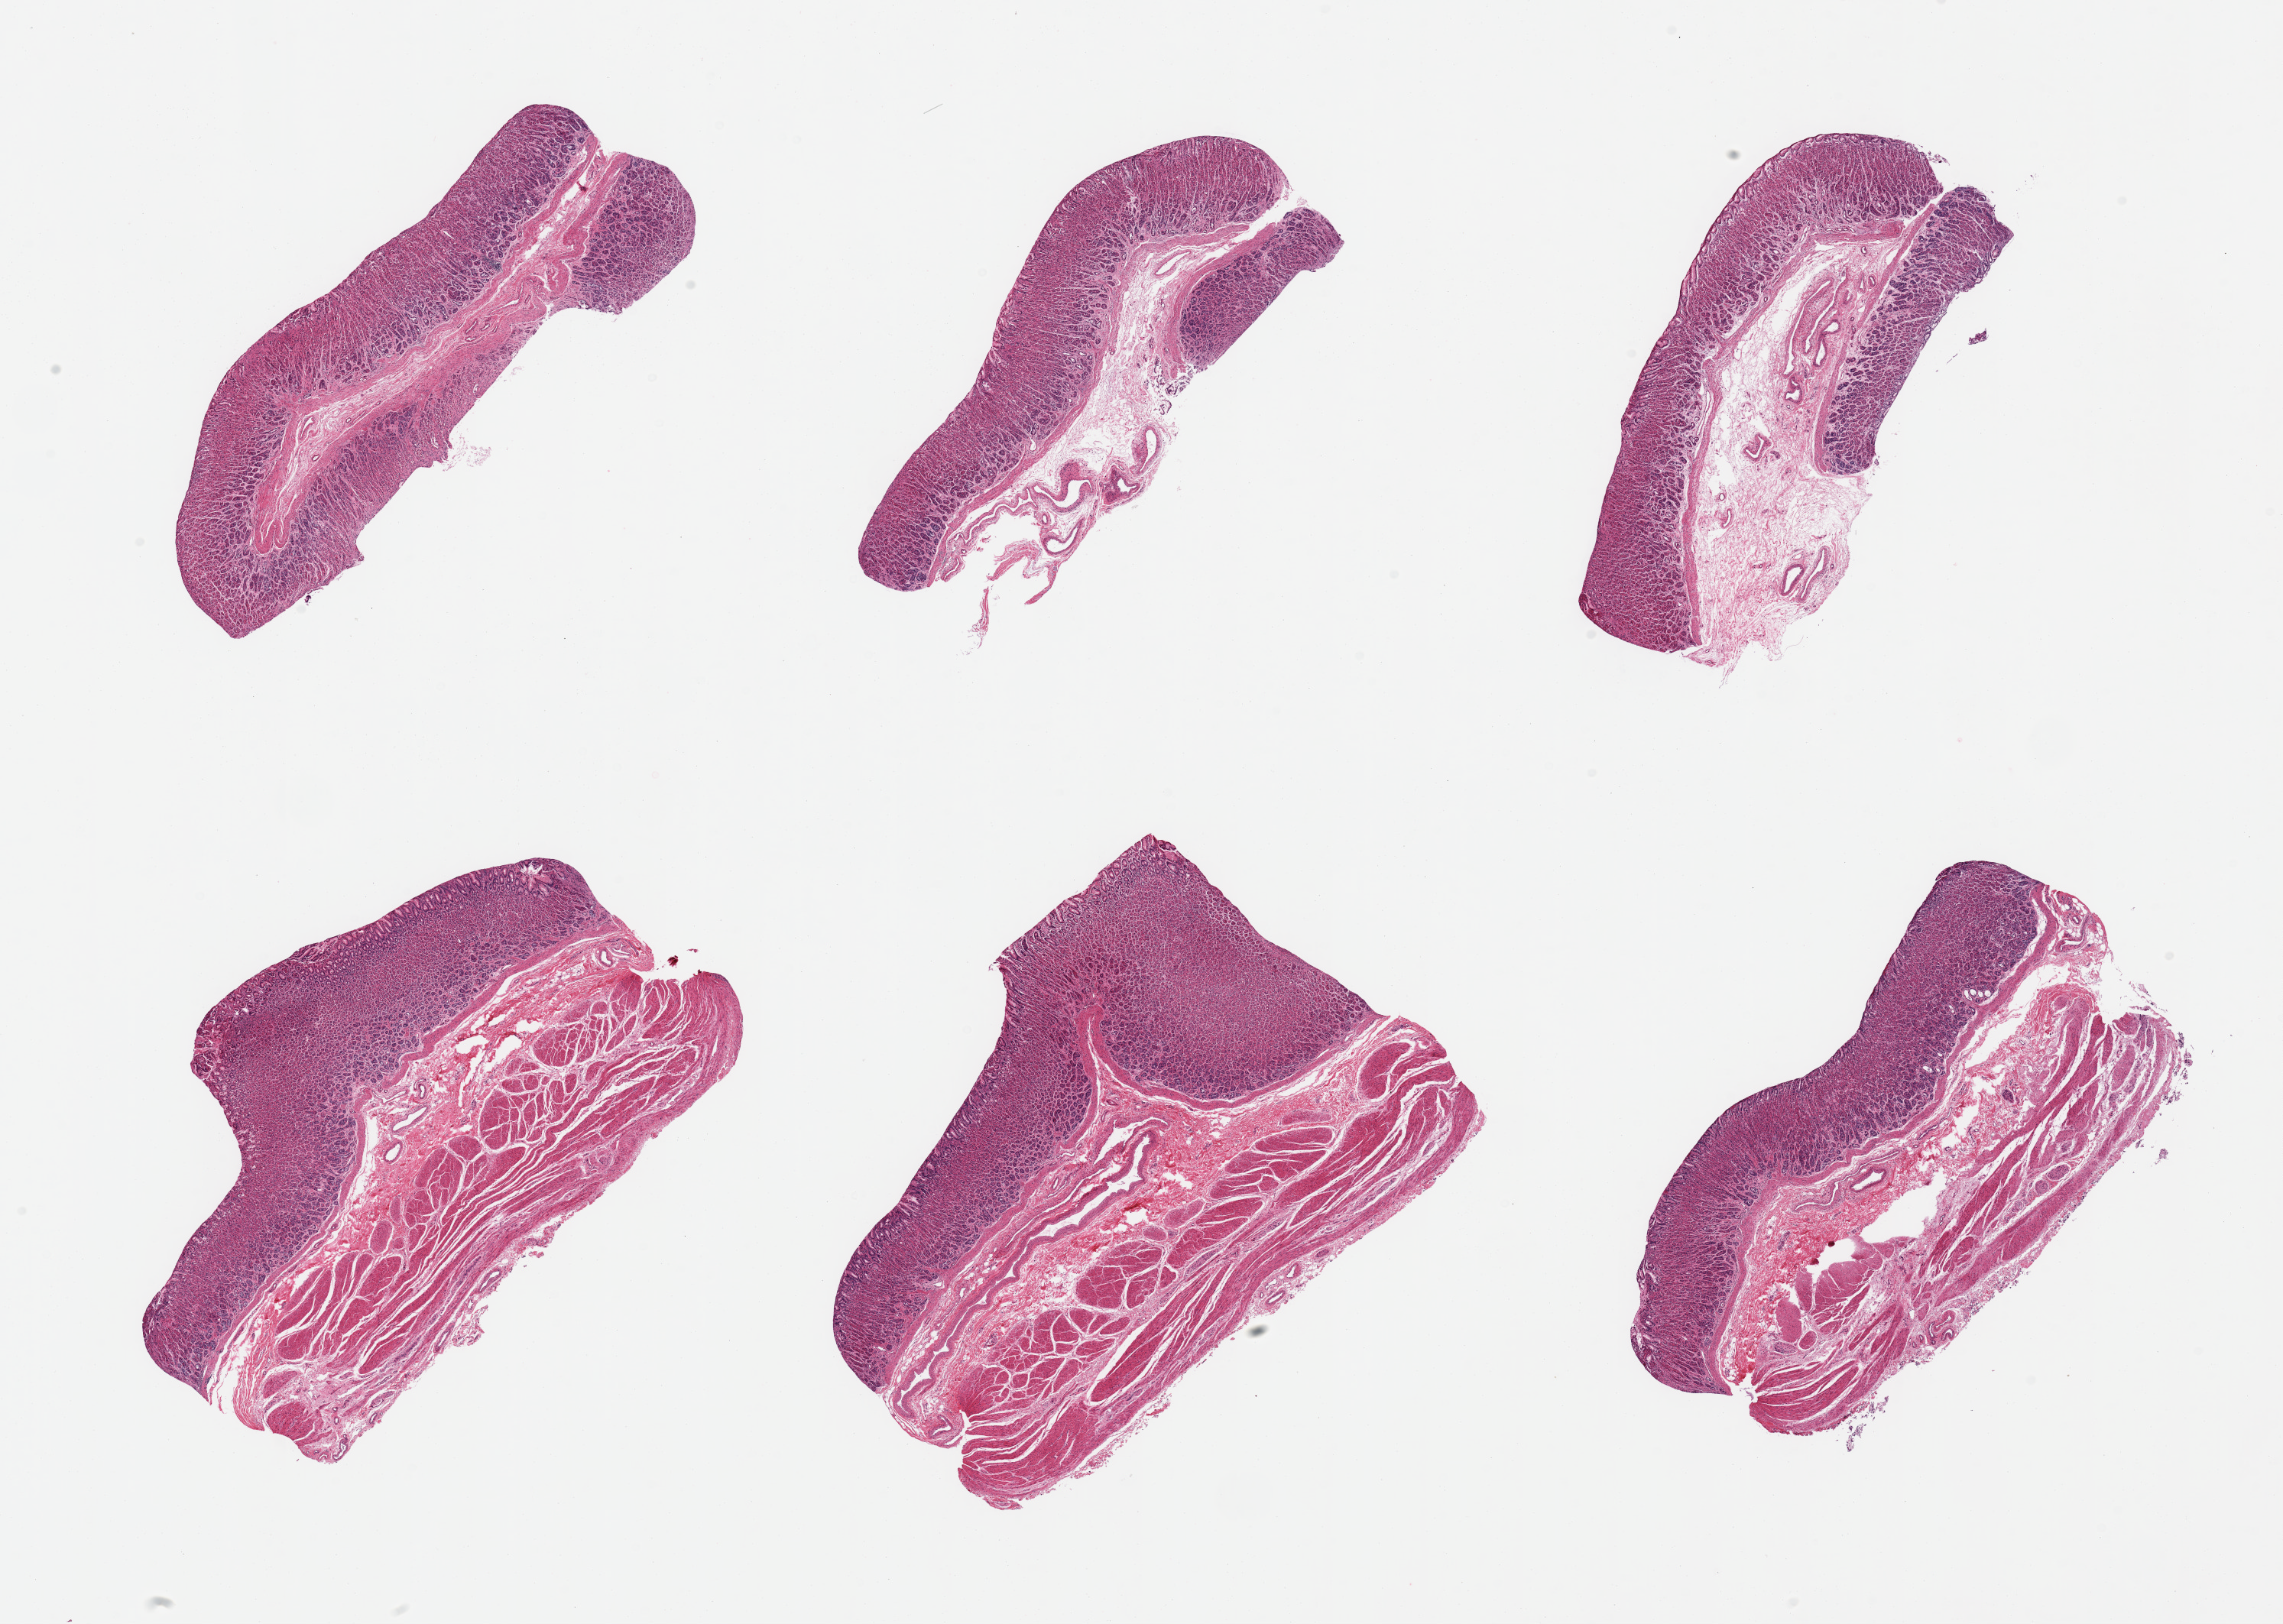
Digitized hematoxylin and eosin (H&E)-stained section, whole scanned area (about 23.6 x 16.8 mm, slide scanned at 20x) shown as a low-resolution overview, PAXgene-fixed, paraffin-embedded tissue, target tissue: stomach, tissue donor sample. Male donor.
- reviewer comment on this tissue sample: 6 pieces, mucosa very well preserved, valuable specimen, up to ~1mm, 30-90% of thickness